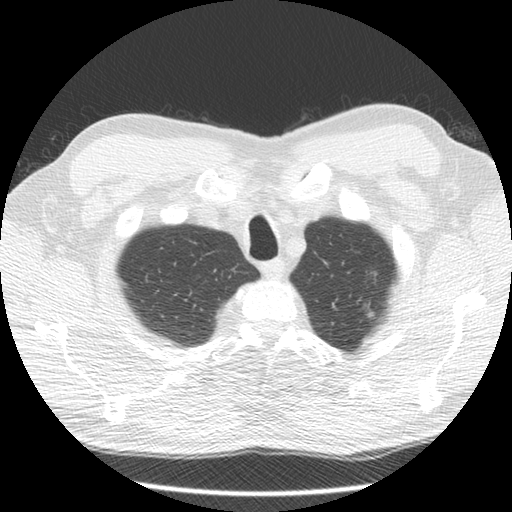
Low-dose screening chest CT, one axial slice; position 120 of 132 along the scan axis; reconstruction kernel STANDARD; 120 kVp; lung window (W 1500 / L -600 HU); 2.5 mm slice thickness; 512 × 512 image matrix, field of view 340 × 340 mm.
Outlined on this slice (expert manual segmentation):
- lesion 1 (tumor, upper lobe of left lung): box from (x=375, y=273) to (x=377, y=276) px